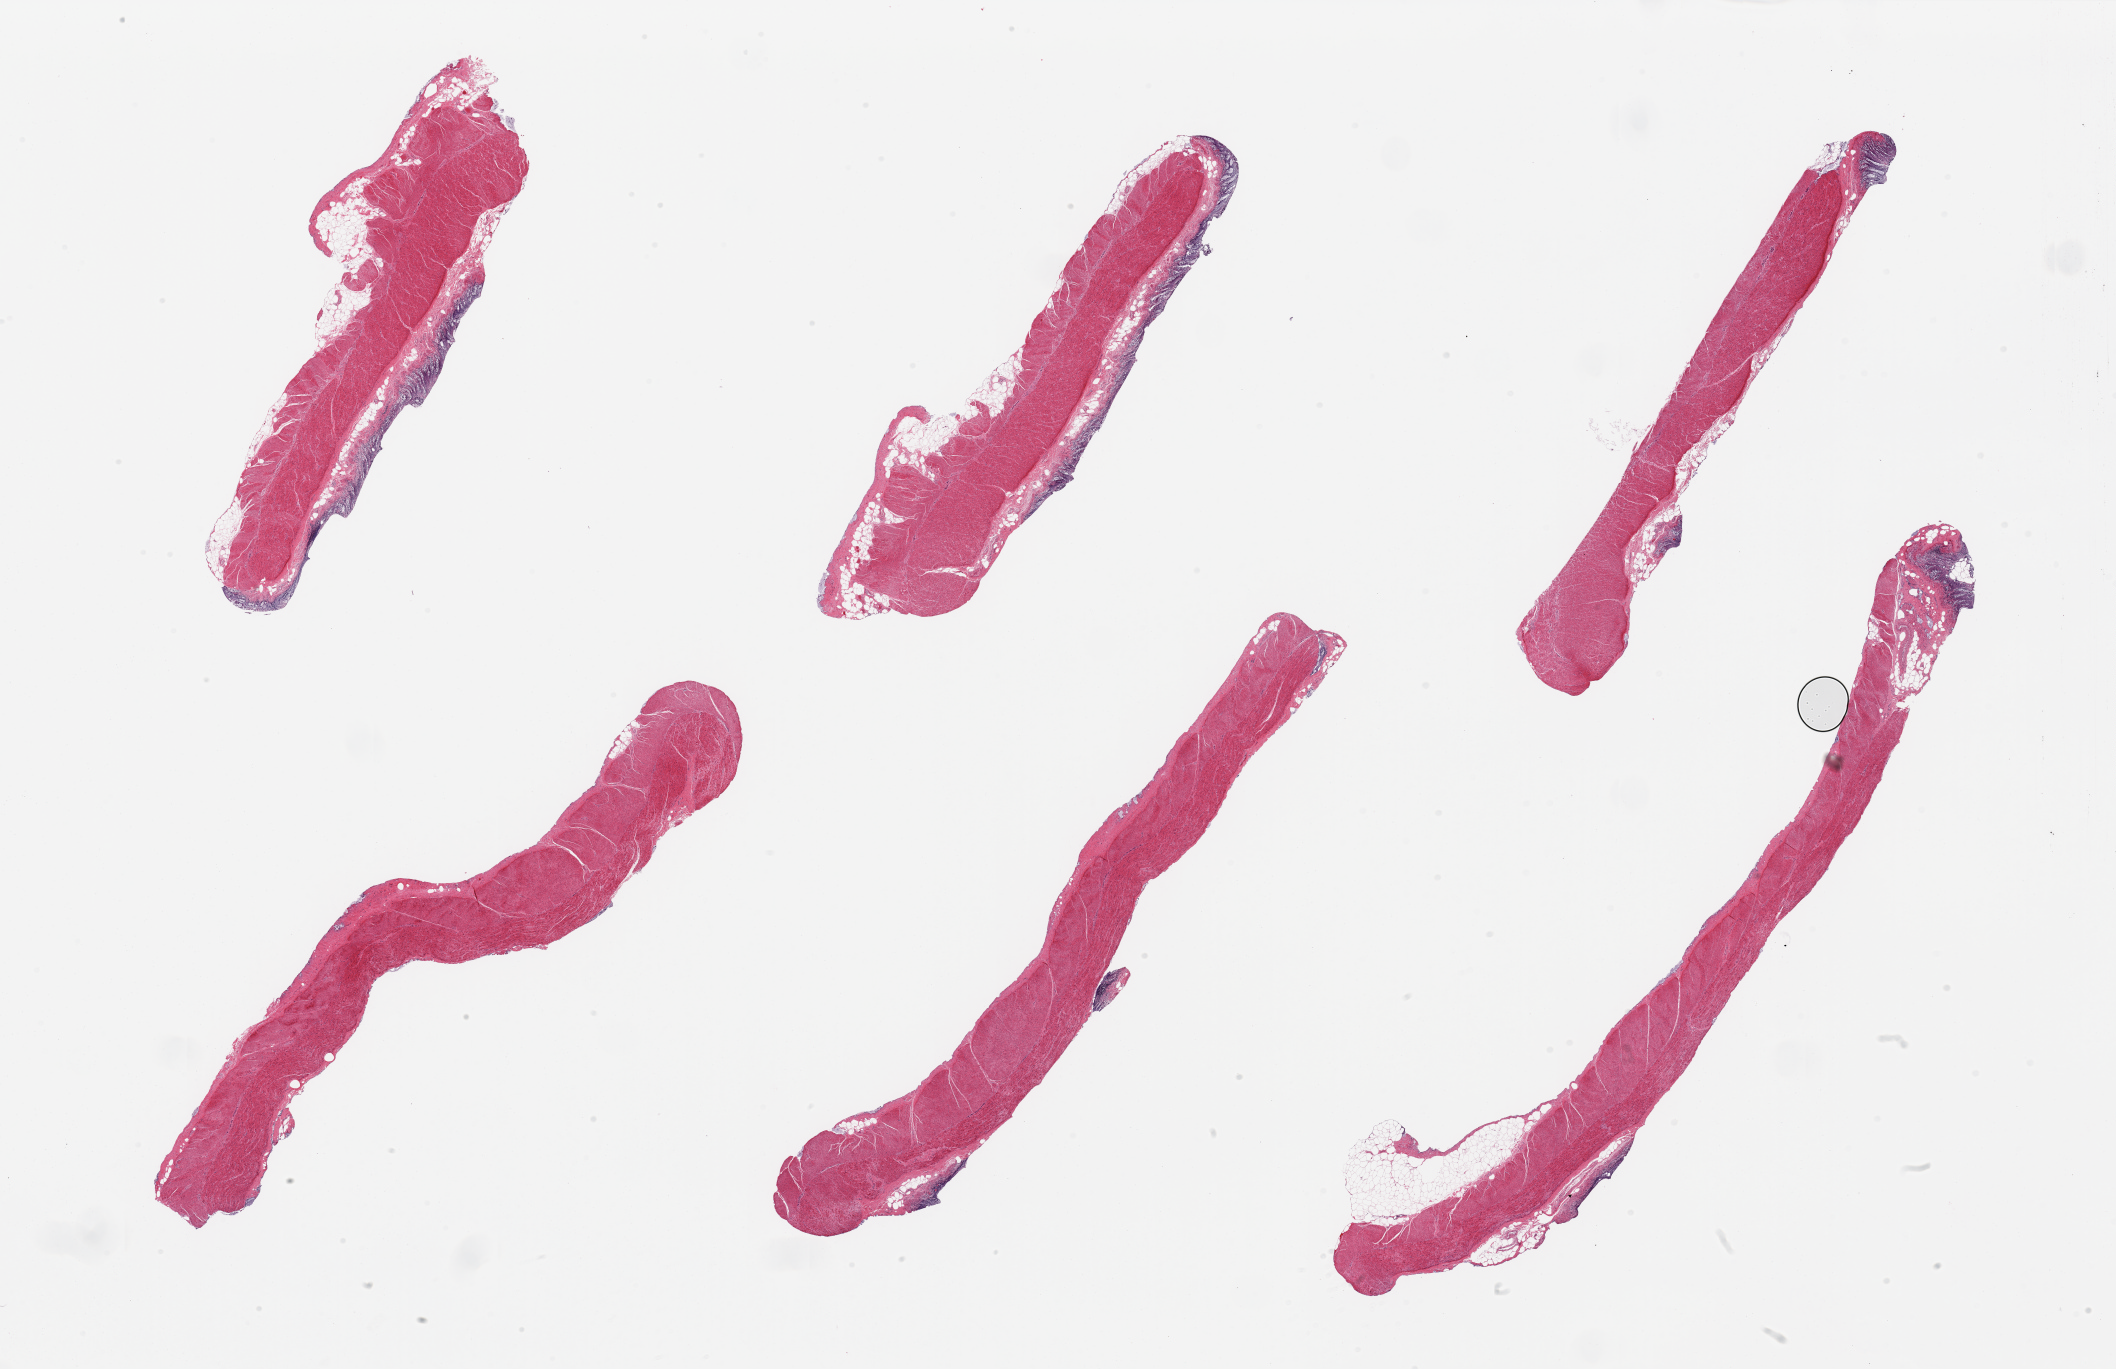
Whole-slide image, haematoxylin and eosin stain — whole scanned area (about 33.5 x 21.7 mm) shown as a low-resolution overview, PAXgene-fixed, paraffin-embedded tissue, sampled site (target tissue): sigmoid colon, tissue donor sample. Male donor.
Pathologist's review note for this sample: 6 pieces, trace contaminant autolyzed mucosa.